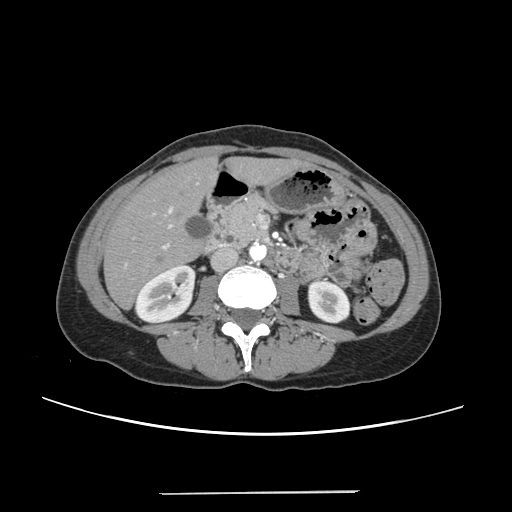
Contrast-enhanced abdominal CT, one axial slice; position 94 of 240 along the scan axis; 120 kVp; intravenous contrast given; soft-tissue window (W 400 / L 40 HU); 1.25 mm slice thickness; 512 × 512 image matrix. Female patient, age 60 years. From the clinical record (not read from this slice): diagnosis: colorectal cancer liver metastases, imaged before liver resection; multiple liver metastases: no; largest metastasis: 1.5 cm; disease in both lobes: no.
Structures marked on this image (outlined manually by an expert reader):
- liver: box from (x=106, y=159) to (x=297, y=307) px
- planned liver remnant (the part of the liver to remain after resection): (x=106, y=160)–(x=298, y=307)
- portal vein (with intrahepatic branches): (x=124, y=208)–(x=172, y=268)